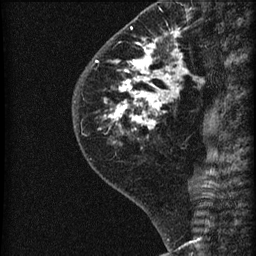
Breast MRI (dynamic contrast-enhanced), one sagittal slice; position 22 of 60 along the scan axis; dynamic contrast-enhanced series, image 2 of 3 at this slice position (ordered by acquisition); 1.5 T; TE 4.2 ms, TR 22.7 ms; 256 × 256 image matrix, field of view 180 × 180 mm. Patient: female, 45 years. From the clinical record (not read from this slice): setting: breast cancer imaged before/during neoadjuvant chemotherapy; receptor status: HR-positive, HER2-negative.
Outlined on this slice (semi-automatically segmented with operator editing):
- analysis volume of interest (the breast-tissue region the enhancement analysis was run in; not a lesion): bounding box [x1, y1, x2, y2] px = [74, 11, 205, 140]
- tumour enhancement mask (voxels above the 90 % enhancement threshold inside the analysis volume of interest): [114, 29, 180, 132]